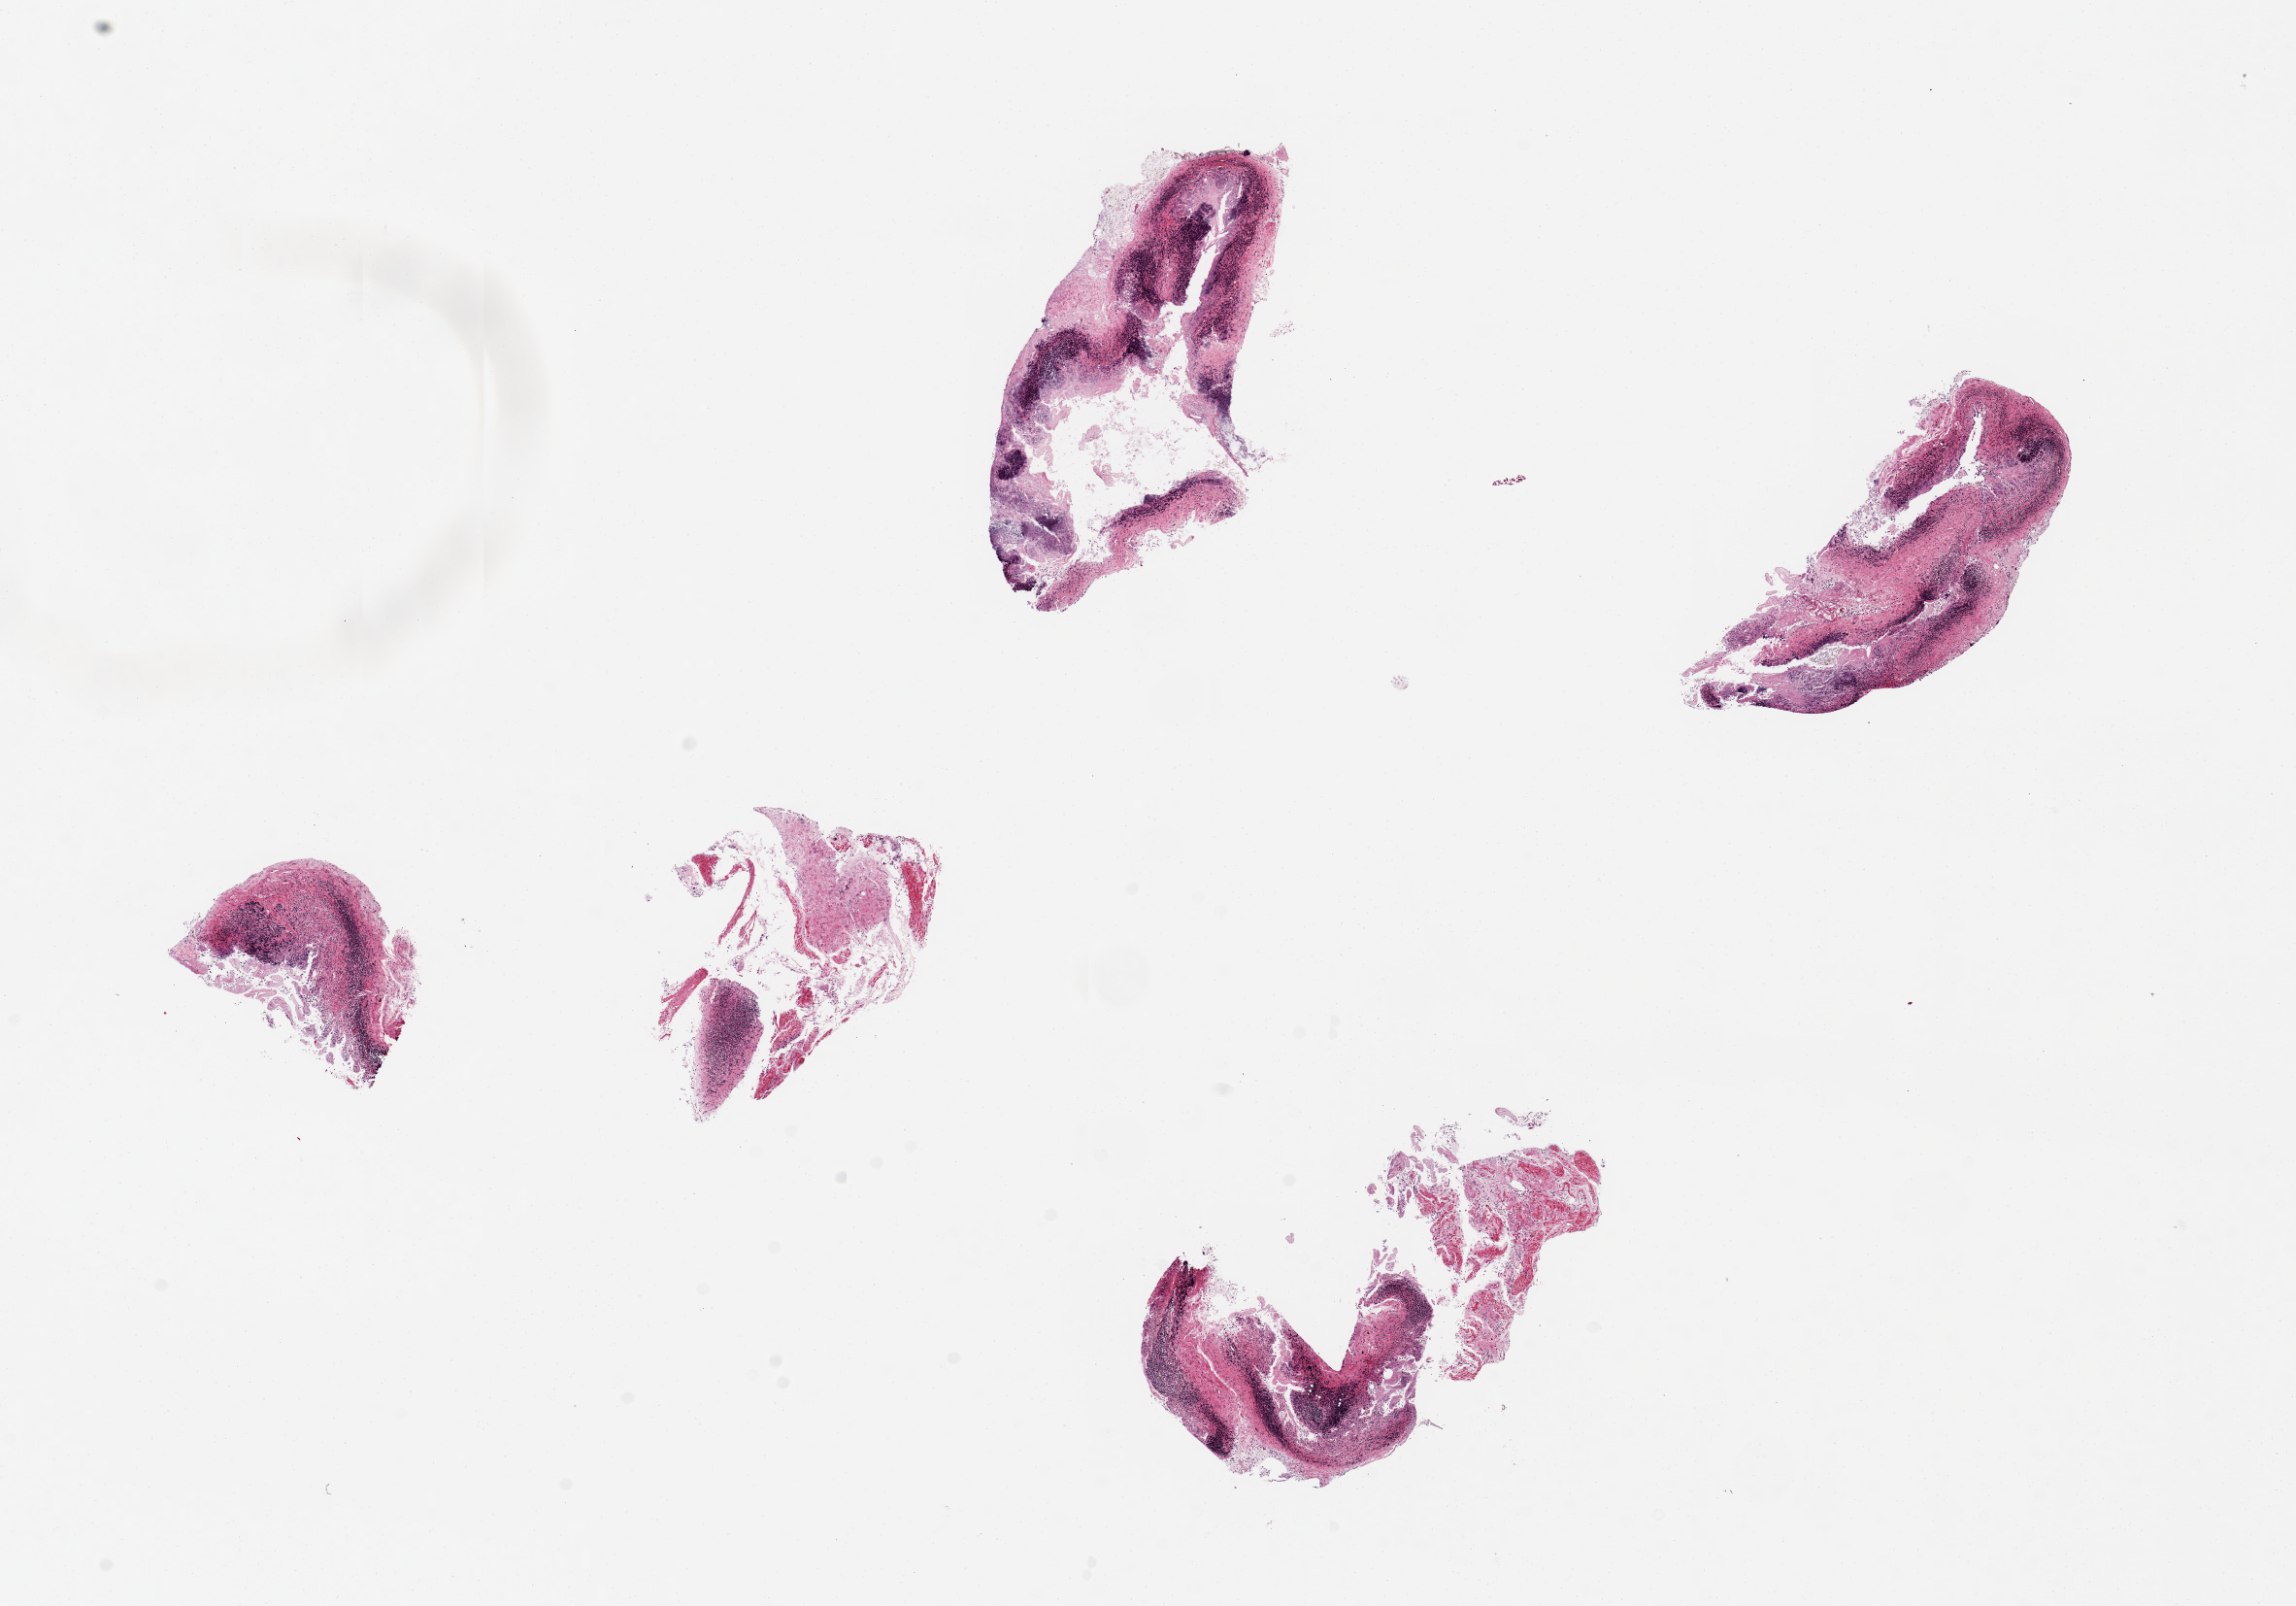
Whole-slide image, haematoxylin and eosin stain — whole scanned area (about 18.7 x 13.1 mm) shown as a low-resolution overview. PAXgene-fixed paraffin-embedded (PFPE) section. Section of ileum (target tissue). Tissue donor sample. Donor: female.
Reviewer comment on this tissue sample: 4 pieces, up to 4x2mm; lymphoid tissue = 2; mucosa = 3; lymphoid tissue in all pieces.